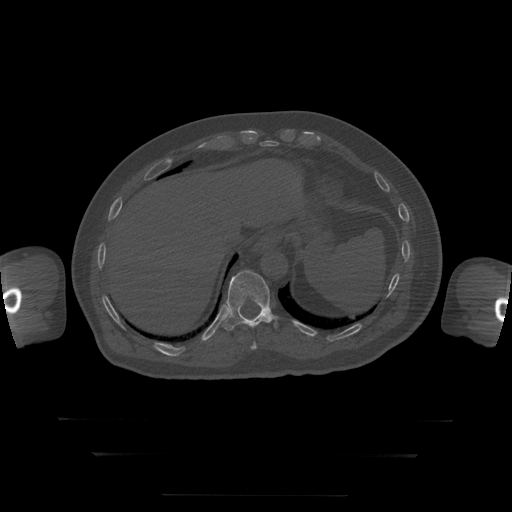
CT including the spine, one axial slice; slice 103 of 397 in the series (ordered by position); bone window (W 1800 / L 400 HU); 512 × 512 image matrix. Patient age 73 years. Case-level facts recorded for this patient, not image findings: primary cancer: prostate.
Annotated regions visible in this slice (semi-automatic segmentation, software-assisted and operator-edited):
- T10 vertebra: bounding box <251,342,257,350> (left, top, right, bottom; pixels)
- T11 vertebra: <223,271,279,331>